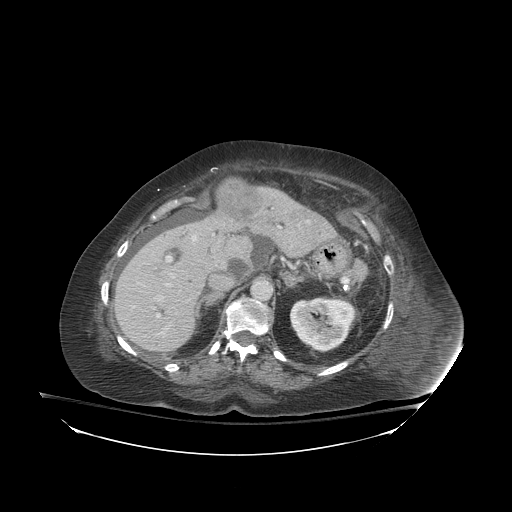
Contrast-enhanced abdominal CT (liver protocol), one axial slice. Slice 54 of 81 in the series (ordered by position). Reconstruction kernel STANDARD. Soft-tissue window (W 400 / L 40 HU). 2.5 mm slice thickness. 512 × 512 image matrix, field of view 500 × 500 mm. Case-level facts recorded for this patient, not image findings: diagnosis: hepatocellular carcinoma (patient treated with transarterial chemoembolisation; whether this scan precedes or follows treatment is not stated here); TNM stage (as recorded): Stage-I; Child-Pugh class: B; tumour differentiation: well-moderately differentiated.
Structures marked on this image (semi-automatic segmentation, software-assisted and operator-edited):
- liver parenchyma outside the tumour (the mass and vessels are separate outlines, so this box may not span the whole liver): bounding box <114,184,334,352> (left, top, right, bottom; pixels)
- mass: <217,178,262,217>
- liver vessels: <133,226,281,329>